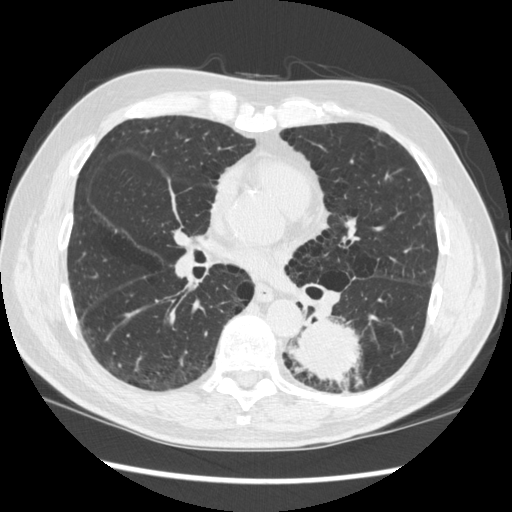
Low-dose screening chest CT, one axial slice. Slice 160 of 348 in the series (ordered by position). Reconstruction kernel STANDARD. 120 kVp. Lung window (W 1500 / L -600 HU). 1.25 mm slice thickness. 512 × 512 image matrix.
Outlined on this slice (expert manual segmentation):
- lesion 1 (tumor, lower lobe of left lung): box from (x=289, y=319) to (x=362, y=386) px